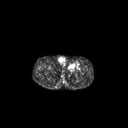
FDG PET of an extremity soft-tissue mass (from a PET/CT study), one axial slice; slice 265 of 267 in the series (ordered by position); 128 × 128 image matrix, field of view 700 × 700 mm. Patient: male, 63 years. Case-level facts recorded for this patient, not image findings: histological type: pleiomorphic liposarcoma; grade: high; site of the primary tumour: left thigh.
Outlined on this slice (expert contour drawn on MRI and transferred to this co-registered scan by the dataset authors):
- gross tumour volume including surrounding oedema: bounding box [x1, y1, x2, y2] px = [68, 62, 80, 70]
- gross tumour volume (mass): [68, 63, 76, 69]